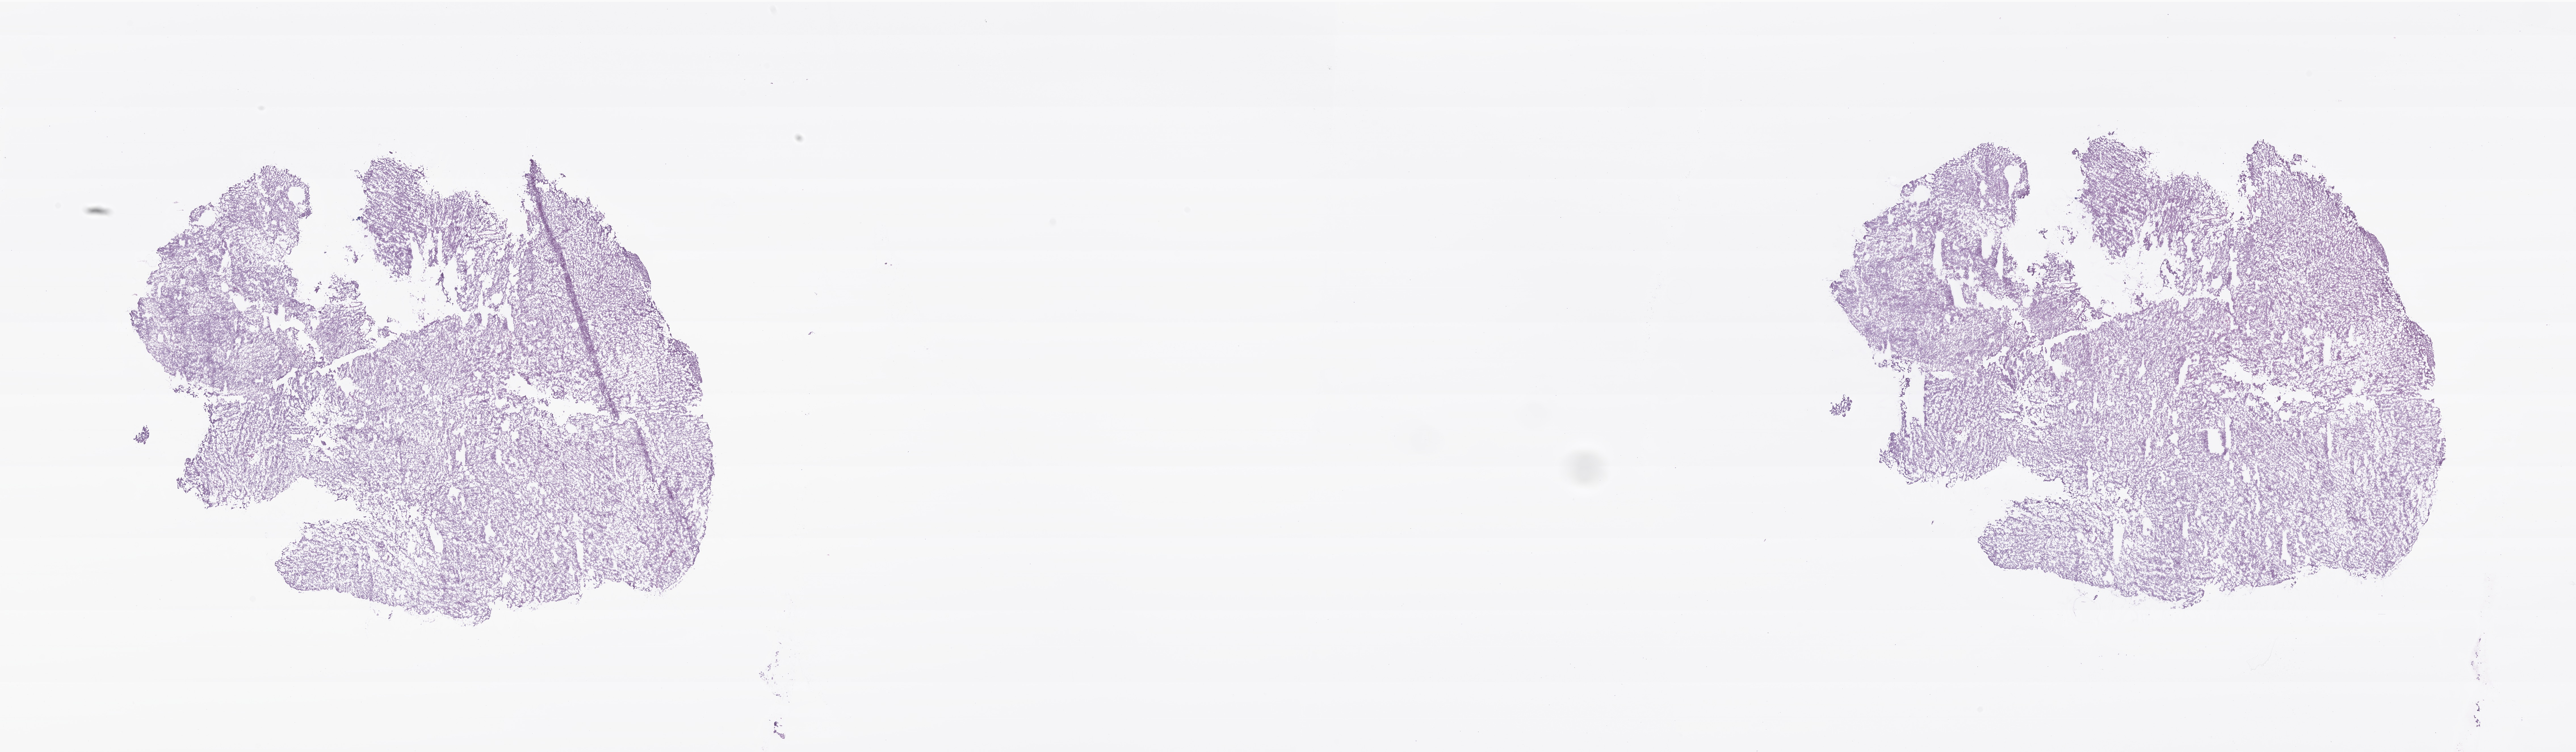
Whole-slide image, H&E stain of tumor tissue from the ovary — whole scanned area (about 38.2 x 11.1 mm) shown as a low-resolution overview. Frozen section. Patient female; age 150 months (12 years 6 months).
Diagnosis (ICD-O-3 morphology term): Sertoli-Leydig cell tumor, poorly differentiated.